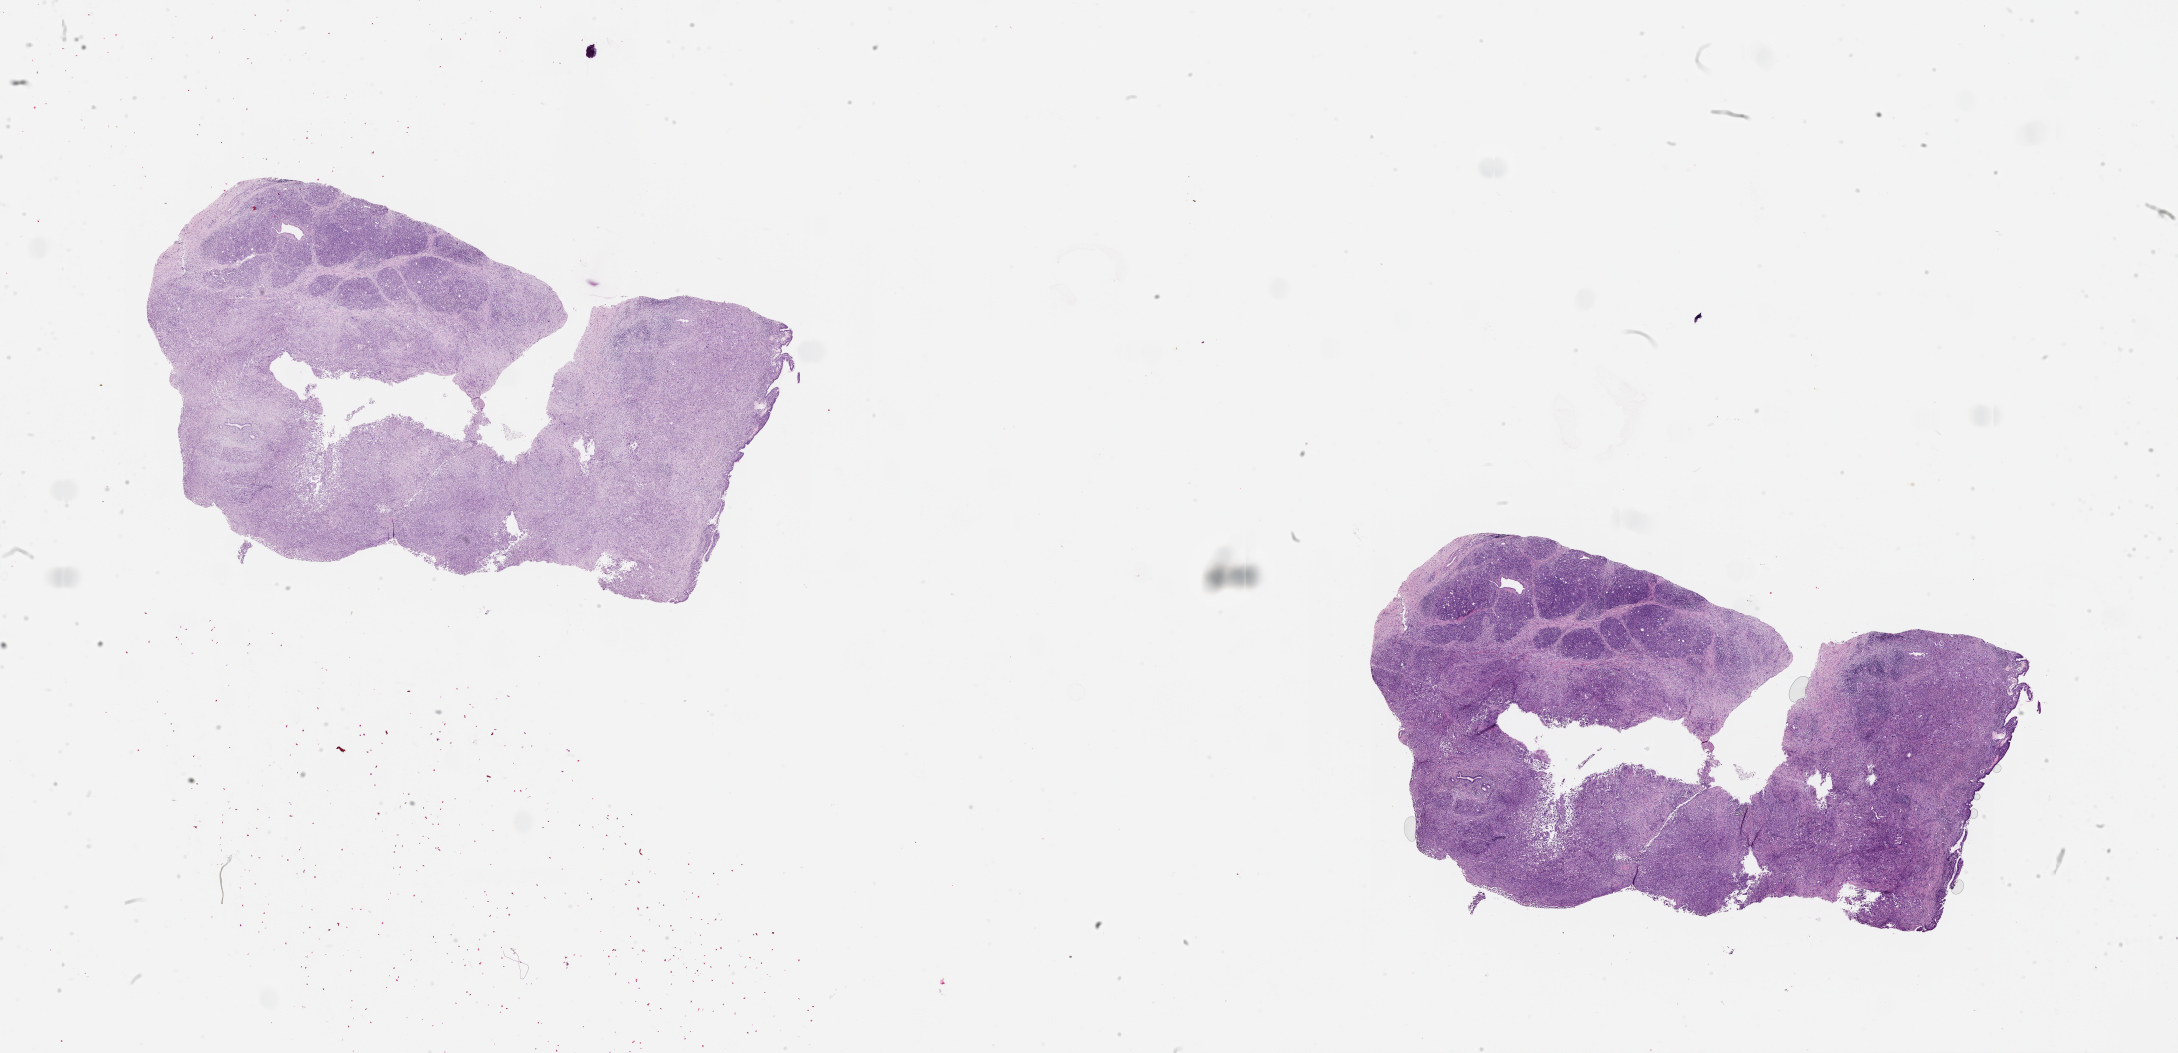
Whole-slide histology image, H&E-stained, a low-resolution overview of the entire scanned area, about 35.1 x 17.0 mm (from a 20x scan); tumour tissue sample, sampled site: pancreas. 69-year-old male patient. Histologic grade: G2 (moderately differentiated). Slide review estimates, as recorded: tumour nuclei 20%, necrosis 0%.
AJCC pathologic stage: IA. Primary tumour site (as recorded): head. Diagnosis: Infiltrating duct carcinoma, NOS.